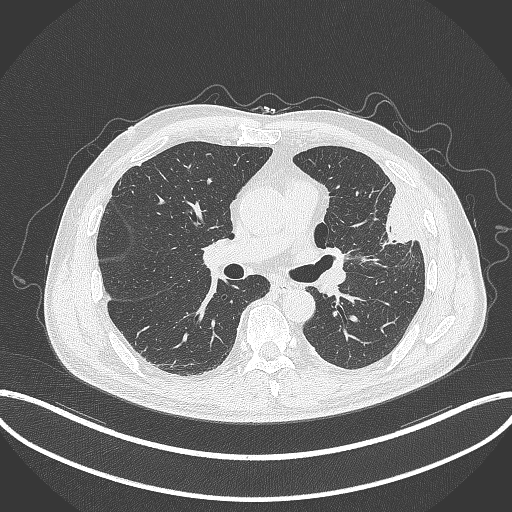
Chest CT, one axial slice; position 186 of 382 along the scan axis; lung window (W 1500 / L -600 HU); 1 mm slice thickness; 512 × 512 image matrix, field of view 415 × 415 mm. Male patient, age 64 years. Case-level facts recorded for this patient, not image findings: clinical TNM (as recorded): T4 N1 M0.
Annotated regions visible in this slice (rectangle marked by the reading radiologist):
- lung tumour (recorded histology: adenocarcinoma): bounding box [x1, y1, x2, y2] px = [370, 193, 422, 253]